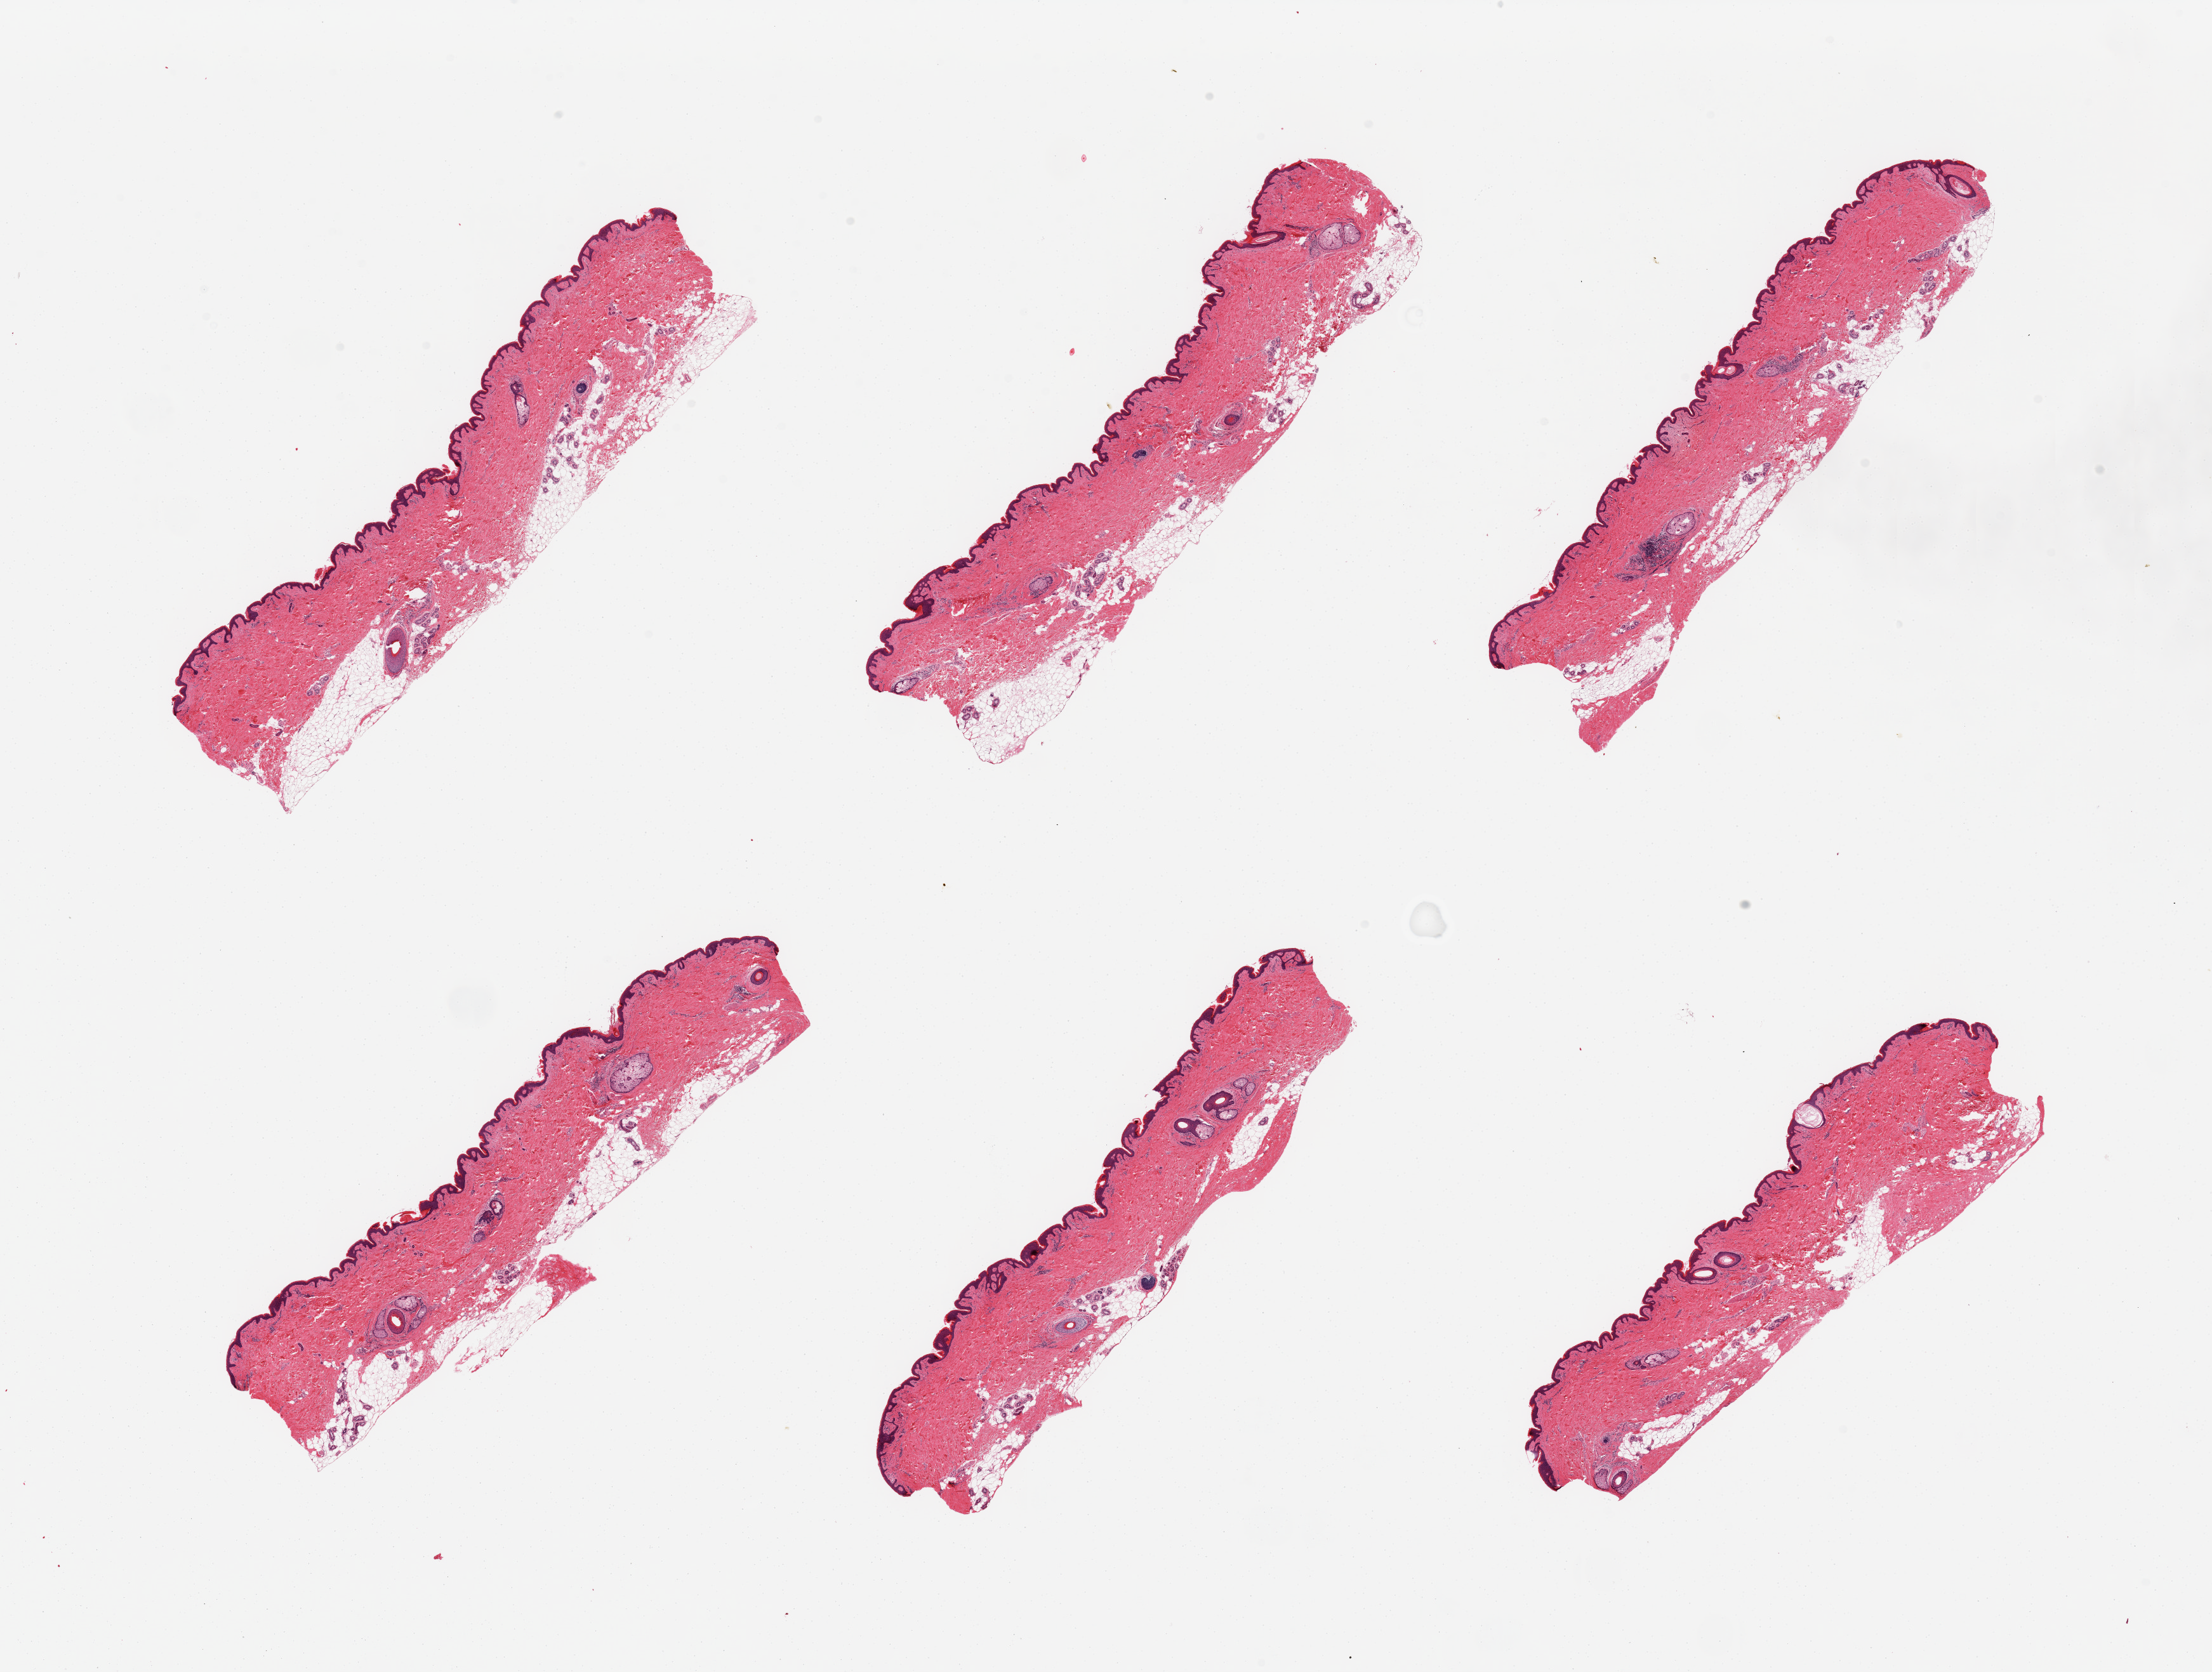
Haematoxylin and eosin whole-slide image, shown as a low-resolution overview of the whole scanned area (about 27.6 x 20.8 mm); PAXgene-fixed, paraffin-embedded tissue; target tissue: skin of suprapubic region; donor tissue sample. Donor: male.
• review note (as recorded): 6 pieces; well trimmed; 10-20% intradermal fat